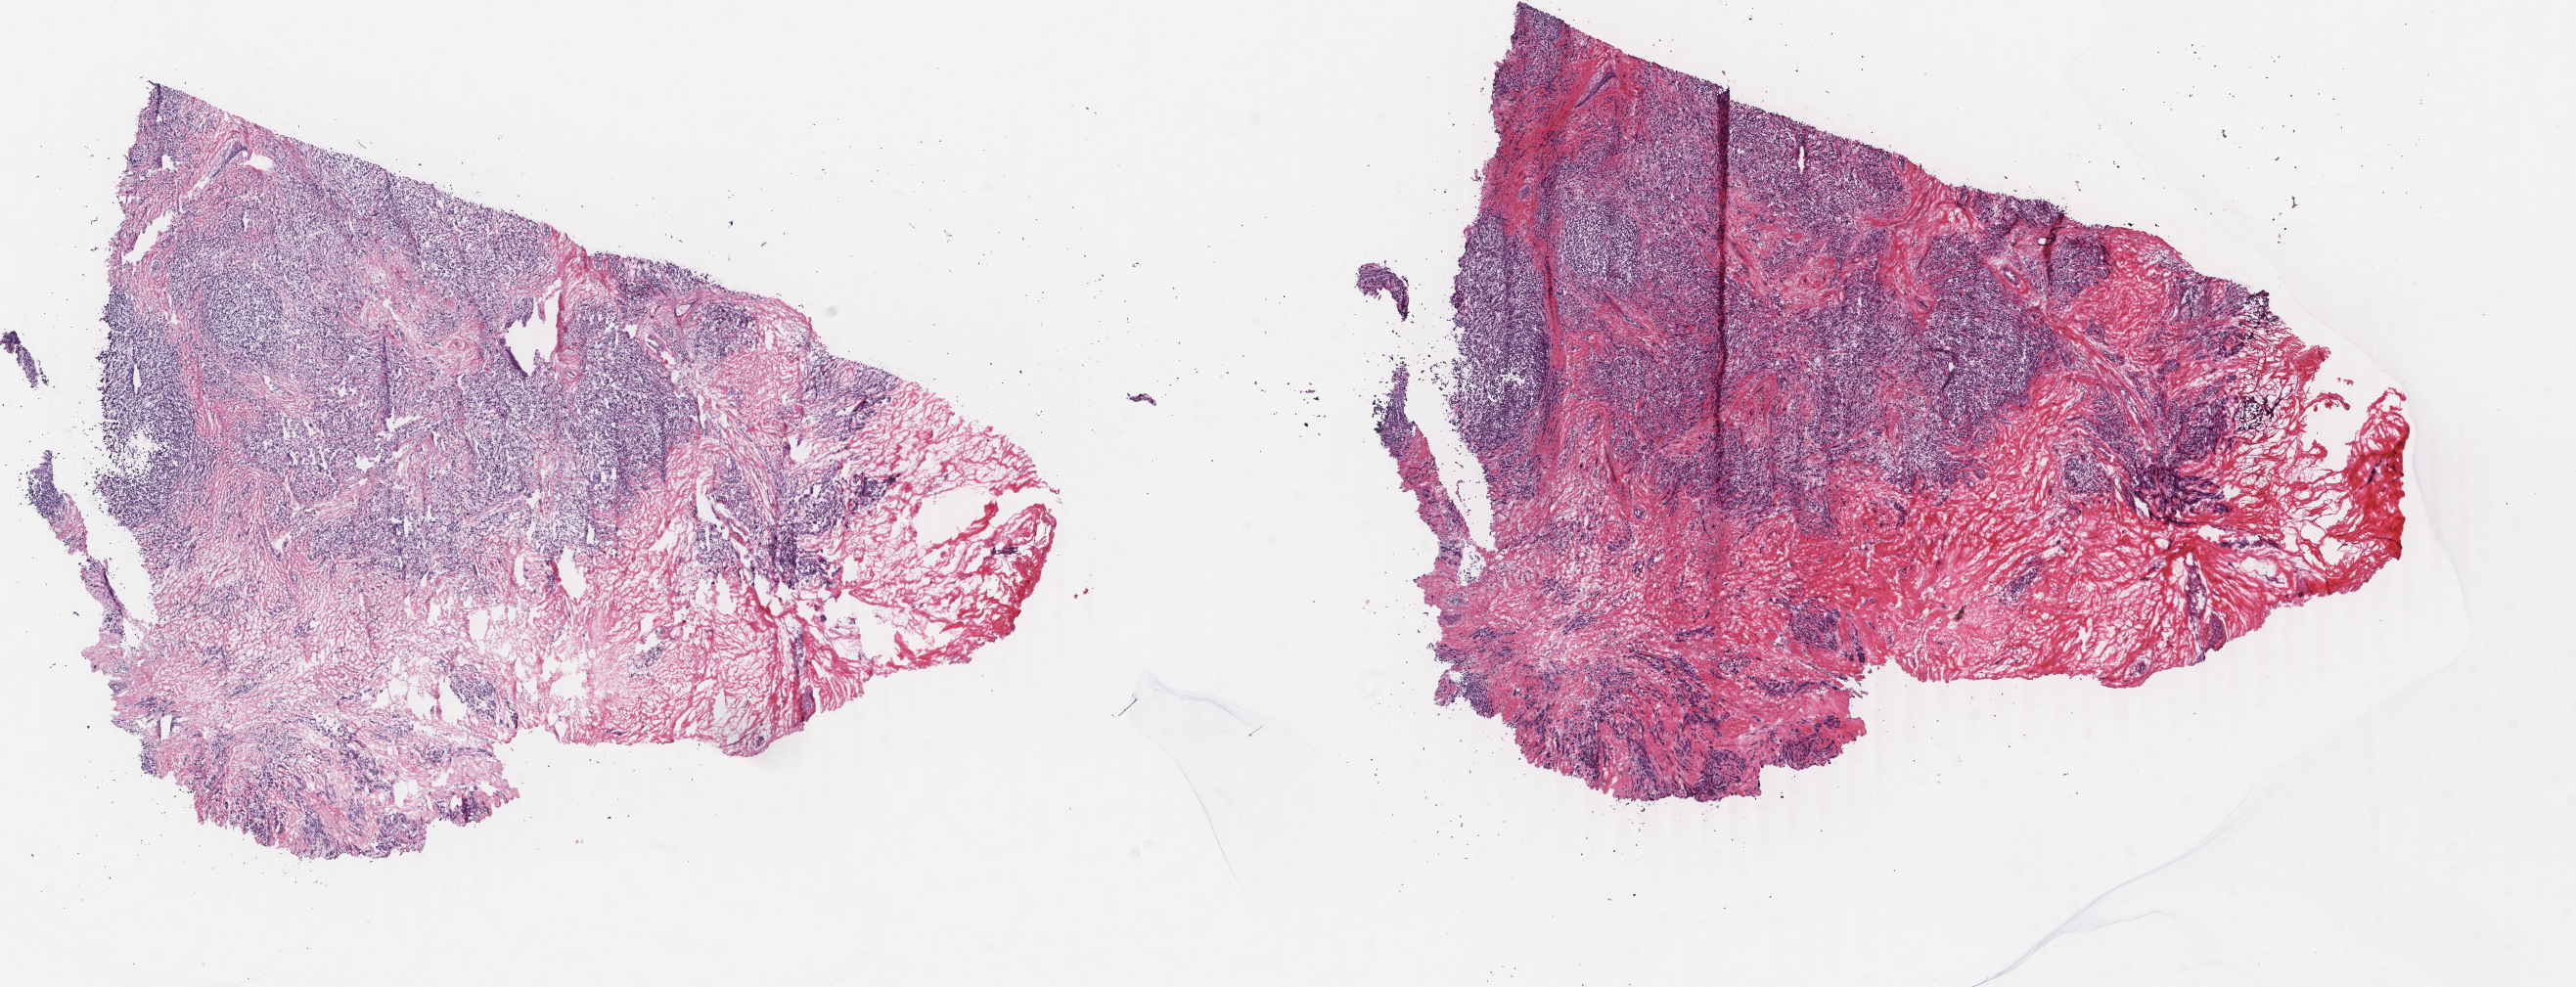
H&E-stained whole-slide image, a low-resolution overview of the entire scanned area, about 20.9 x 8.0 mm (acquisition: 40x scan), frozen section from the top of the tissue portion, primary tumour sample from the breast. Female, age 75 years at initial diagnosis. Composition of this section per pathologist review: tumour cells 80%, tumour nuclei 80%, normal cells 0%, stromal cells 20%, necrosis 0%. Inflammatory infiltration, as recorded: lymphocyte infiltration 2%, monocyte infiltration 1%, neutrophil infiltration 0%.
• TNM: T2 N0 (i+) M0
• AJCC pathologic stage: IIA (6th edition)
• lymph nodes positive (case pathology): 0 of 4 examined
• diagnosis: Pleomorphic carcinoma